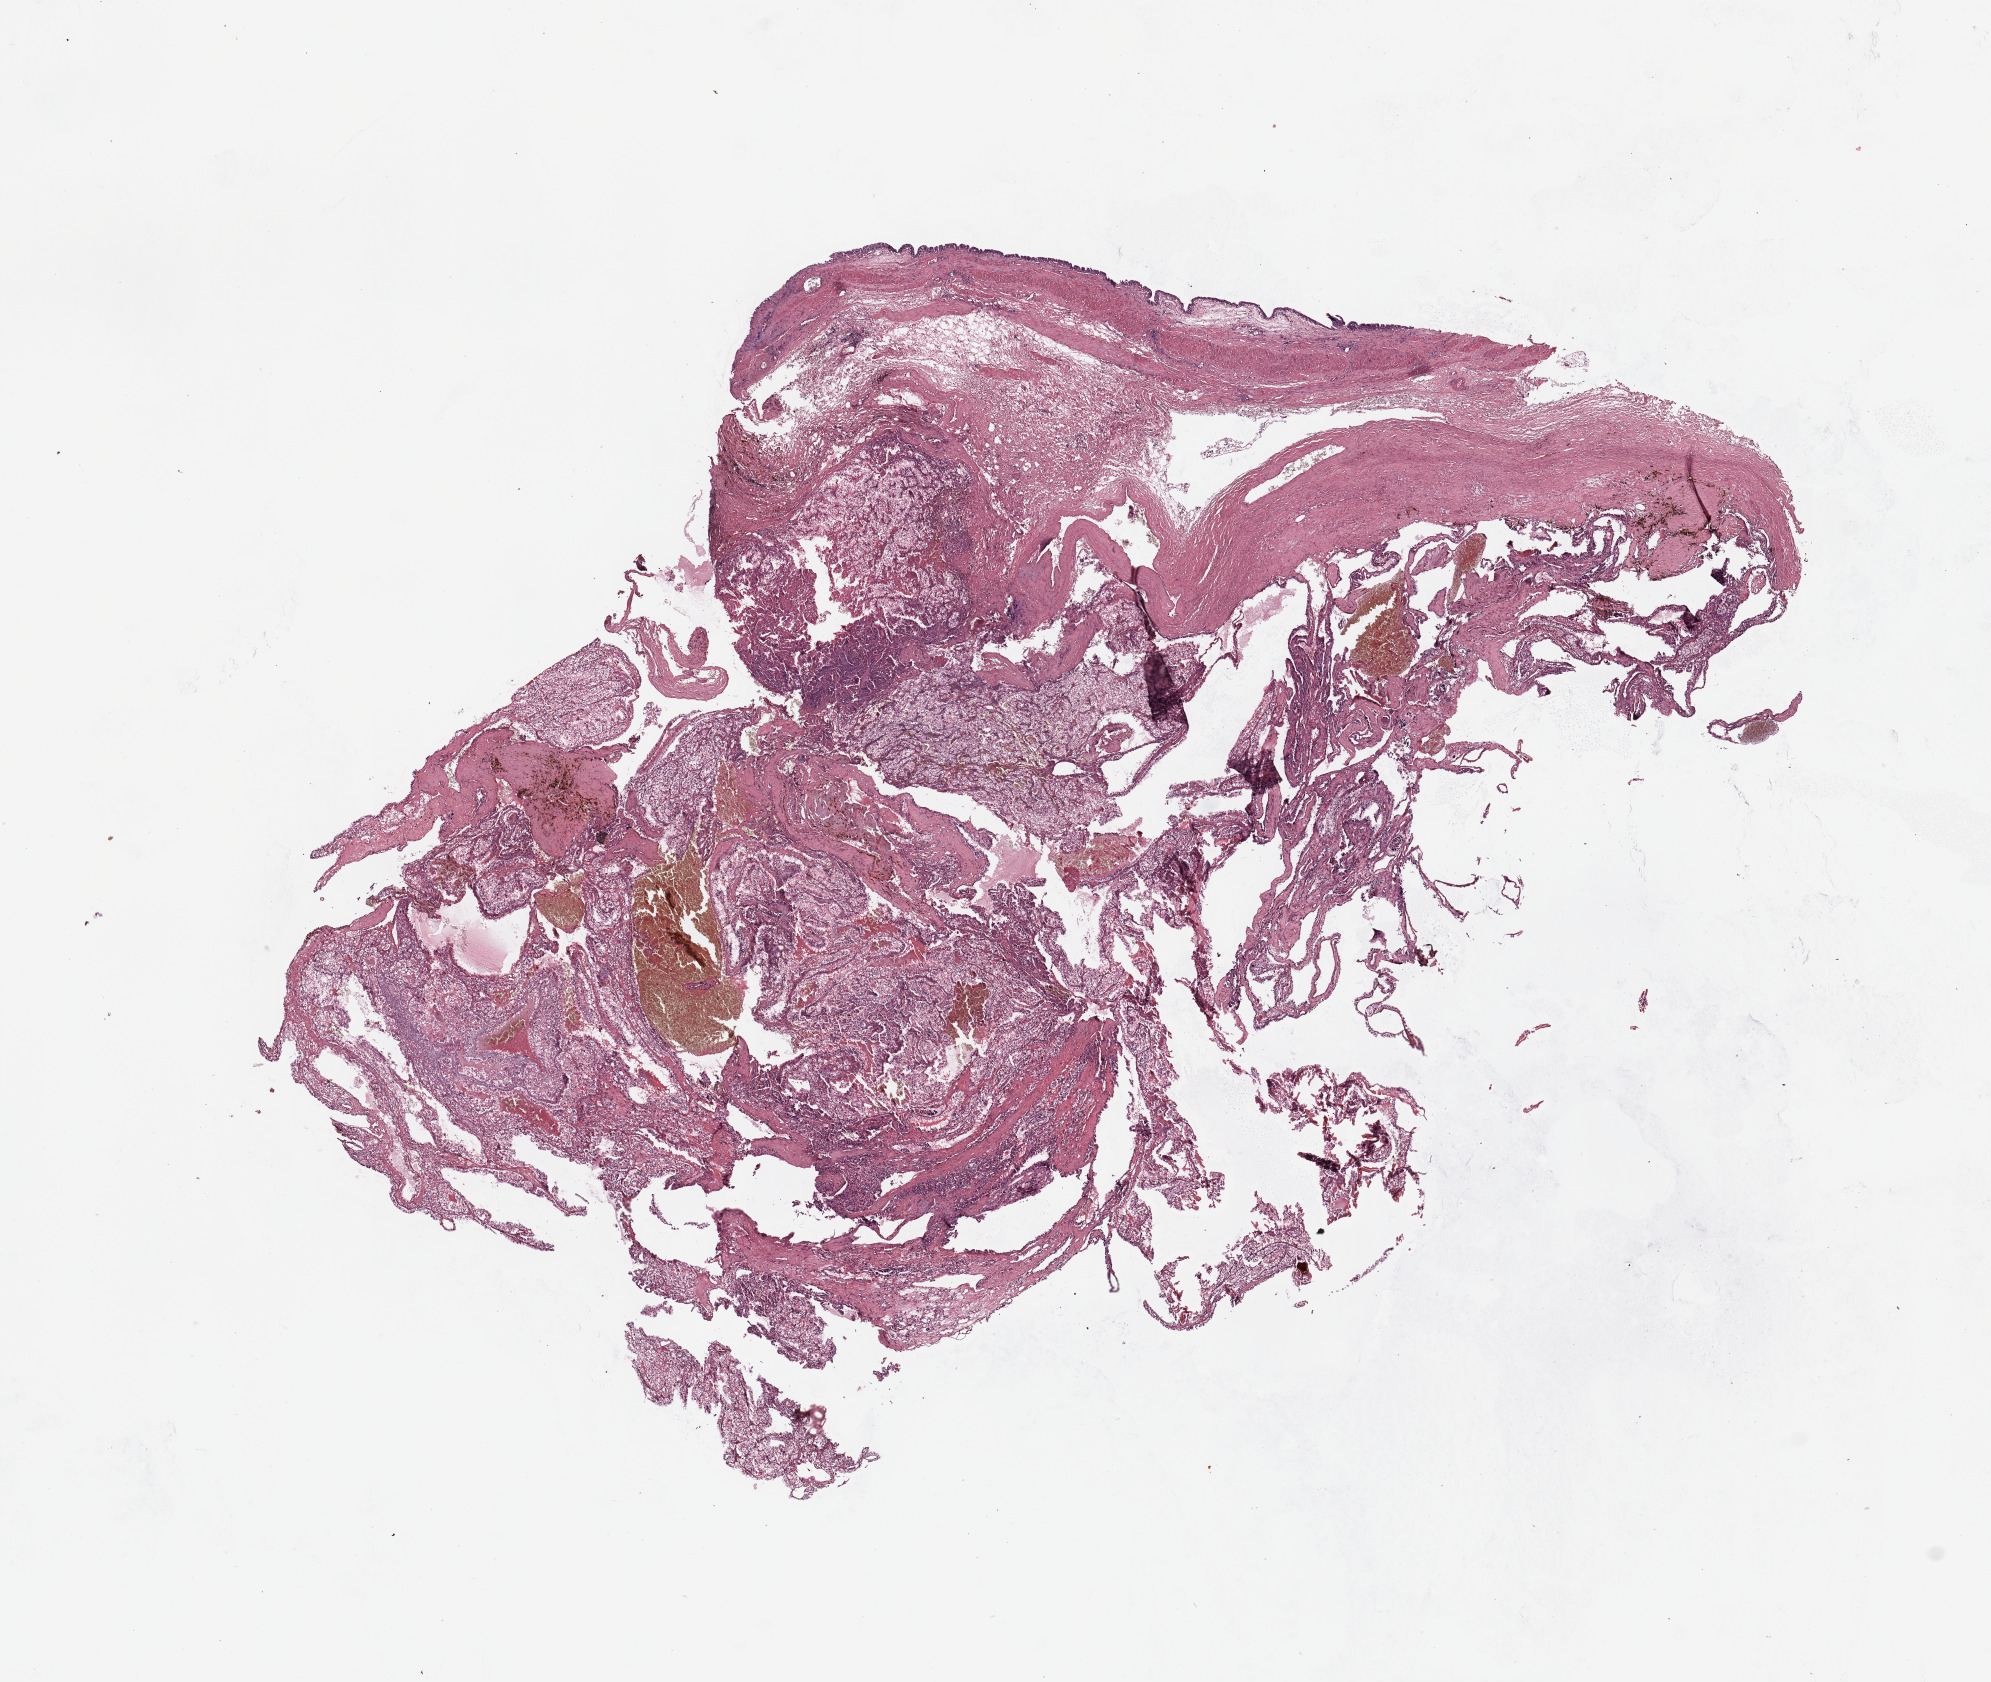
H&E whole-slide image — a low-resolution overview of the entire scanned area, about 15.8 x 13.3 mm (acquisition: 20x scan). Tumour tissue sample, sampled site: kidney. 61-year-old male patient. Histologic grade: G3 (poorly differentiated). Composition of this section per pathologist review: tumour nuclei 80%, necrosis 10%.
• primary tumour site (as recorded): upper pole
• histologic diagnosis: Renal cell carcinoma, NOS
• AJCC pathologic stage: II